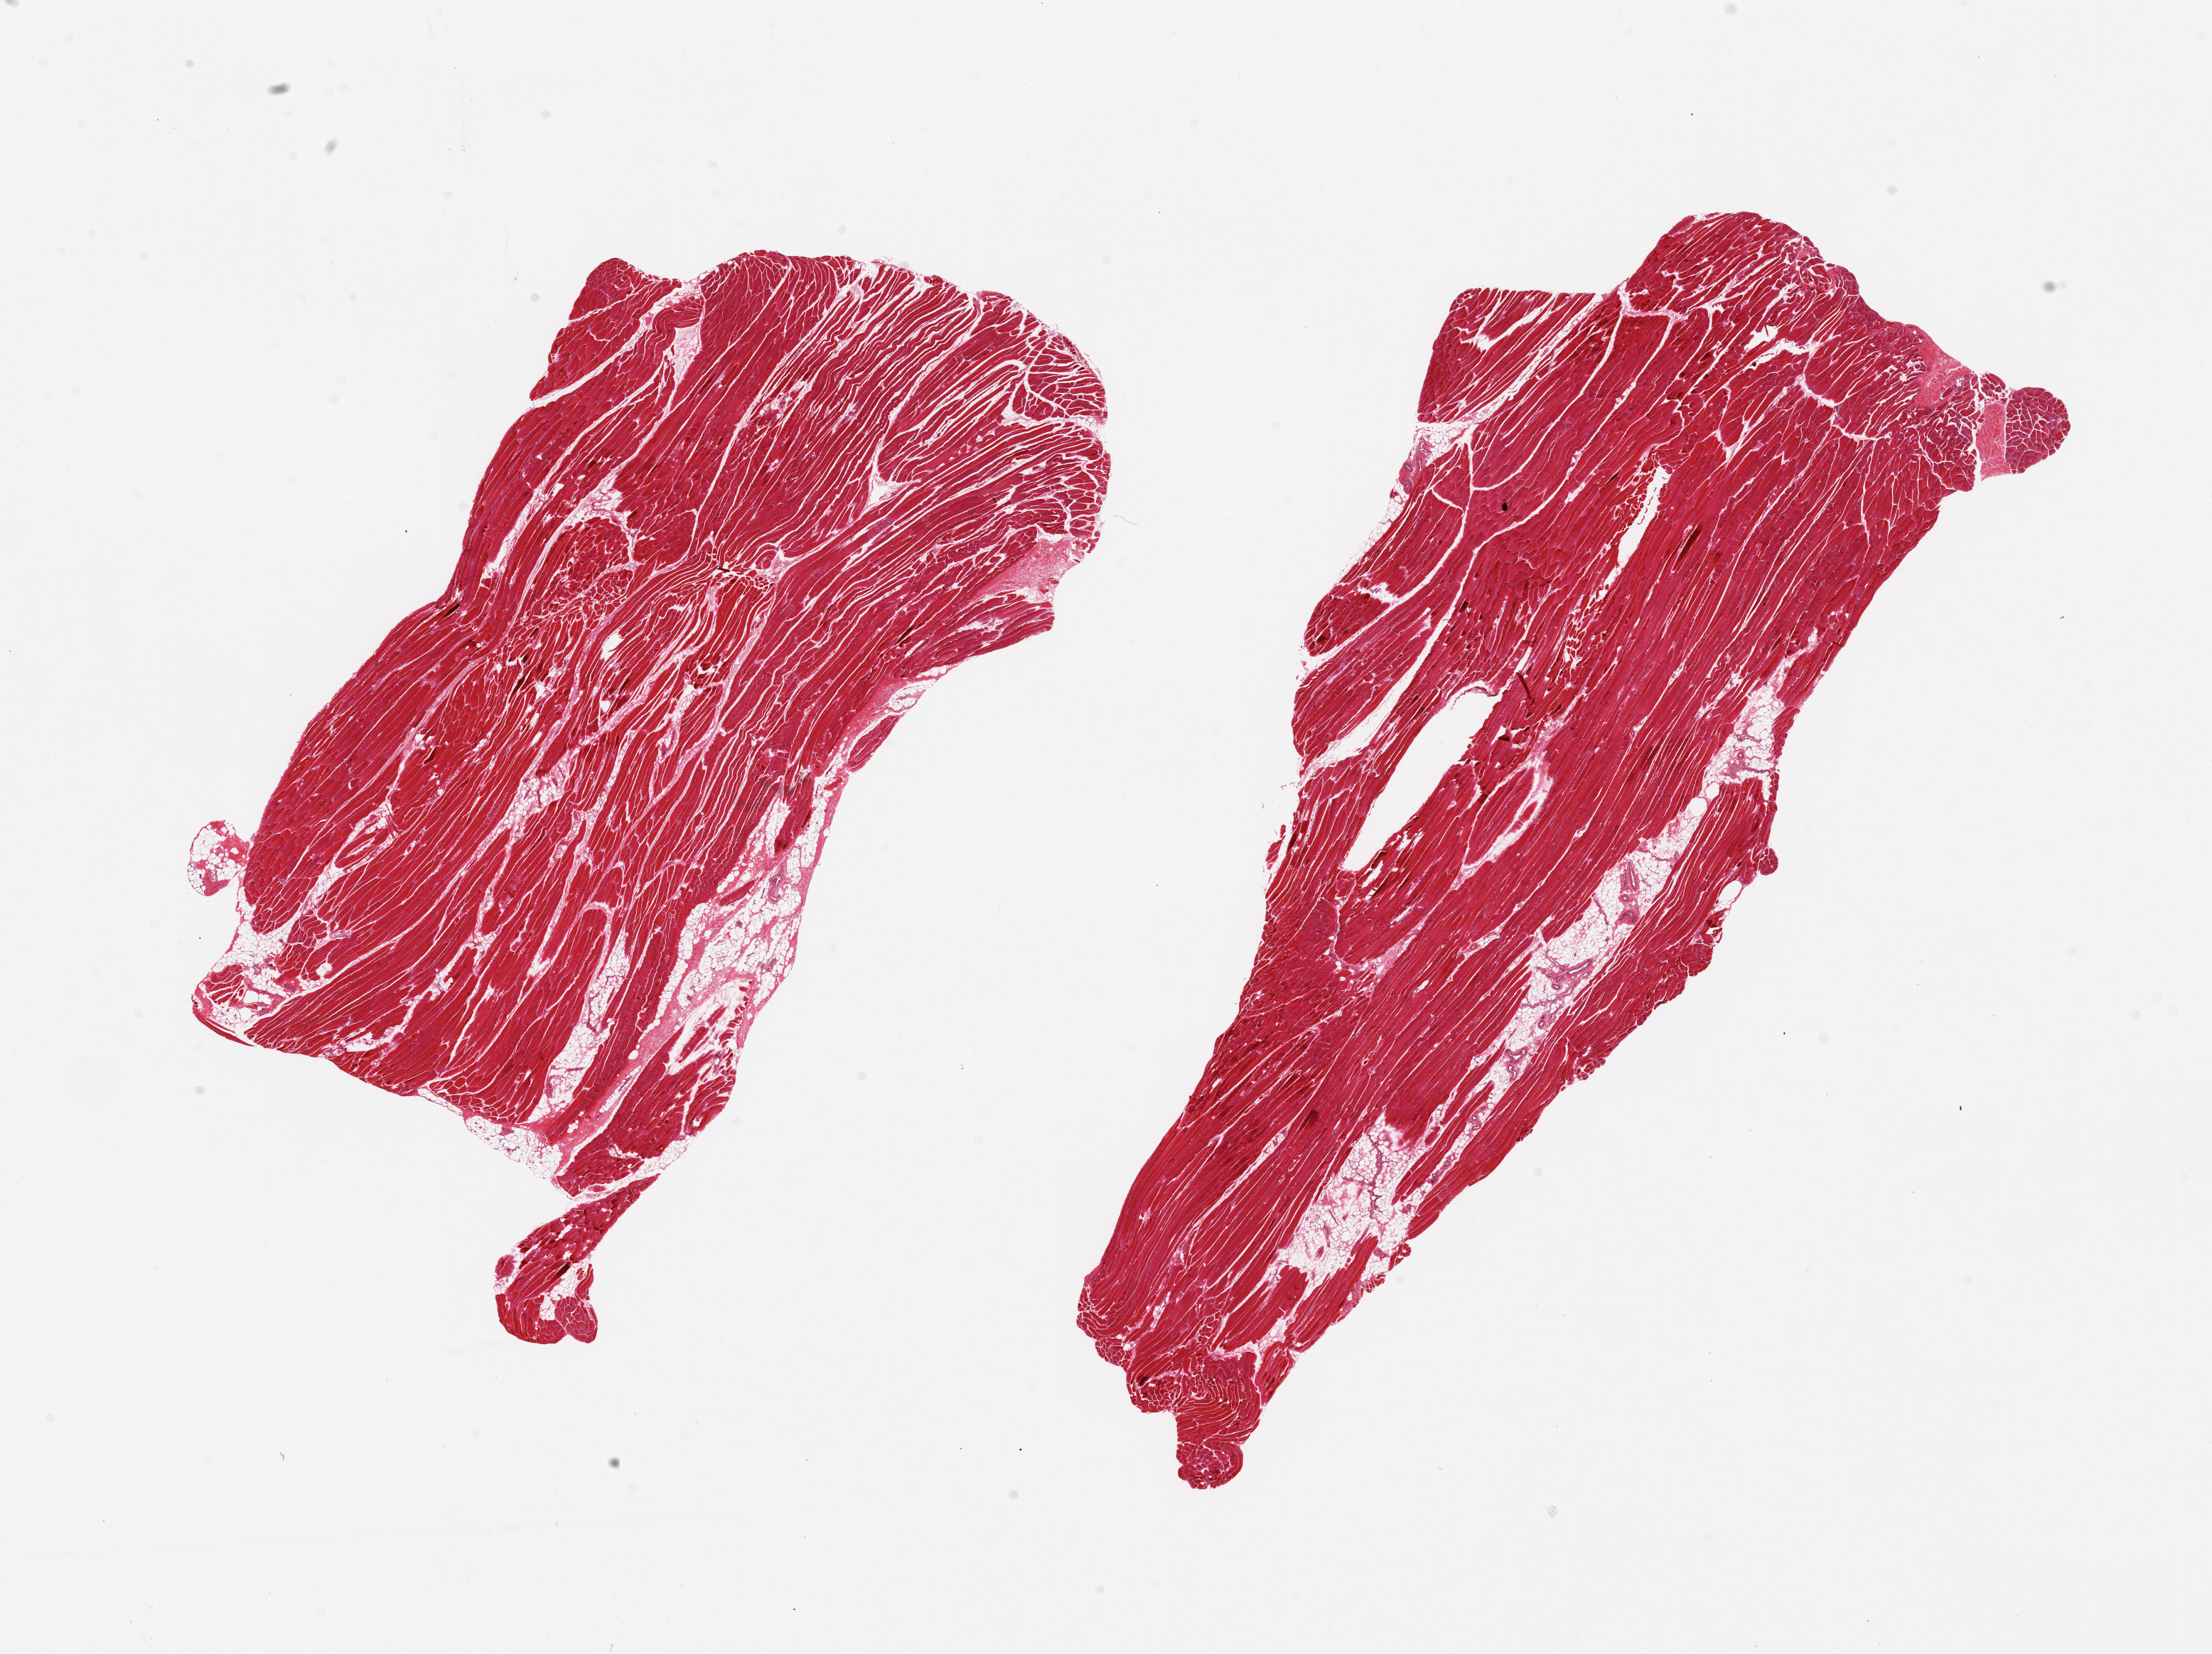
H&E whole-slide image — a low-resolution overview of the entire scanned area, about 24.6 x 18.4 mm. PAXgene-fixed, paraffin-embedded tissue. Section of skeletal muscle (target tissue). Donor tissue sample. Donor: female.
Reviewer comment on this tissue sample: 2 pieces; skeletal muscle with 5-10% internal fat.